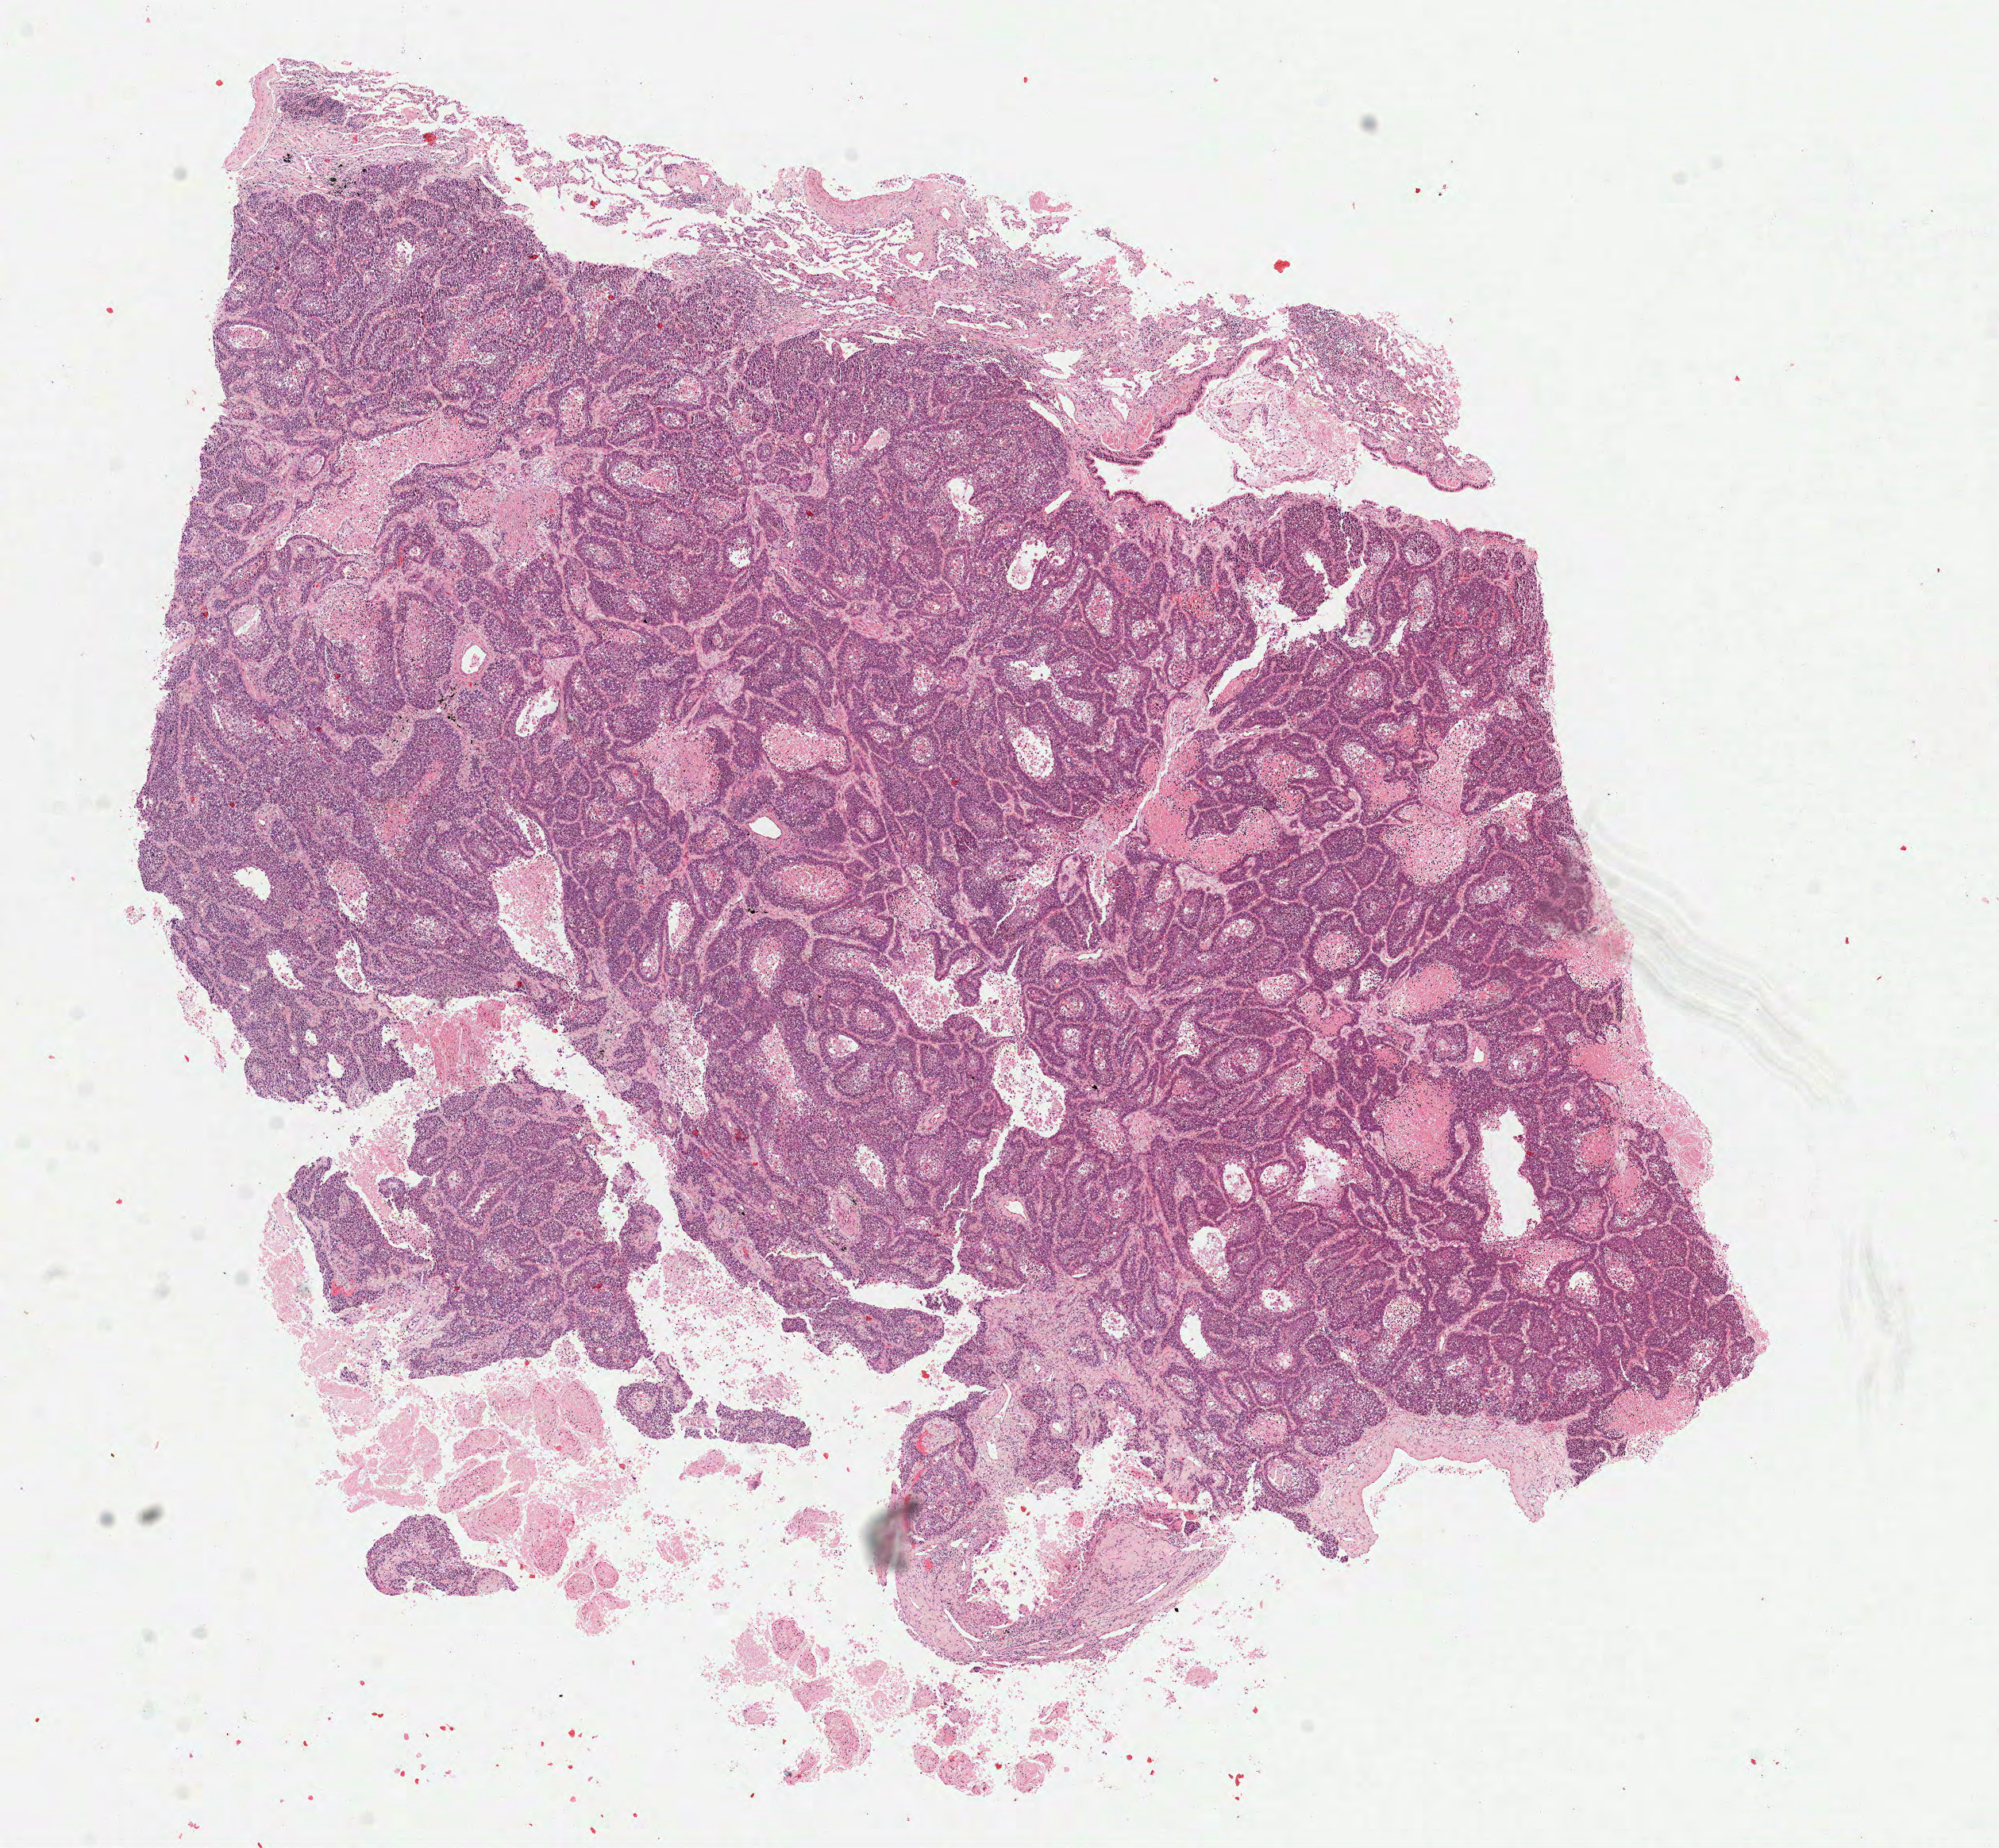
Whole-slide histology image, Hematoxylin and eosin (H&E) stained, whole scanned area (about 10.2 x 9.4 mm, slide scanned at 40x) shown as a low-resolution overview, frozen section from the top of the tissue portion, sample: primary tumour, lung. Patient: male, age at initial diagnosis 81 years. Composition of this section per pathologist review: tumour cells 70%, tumour nuclei 80%, normal cells 5%, stromal cells 10%, necrosis 20%.
* histologic diagnosis: Squamous cell carcinoma, NOS (lower lobe, lung)
* AJCC pathologic stage: IIB